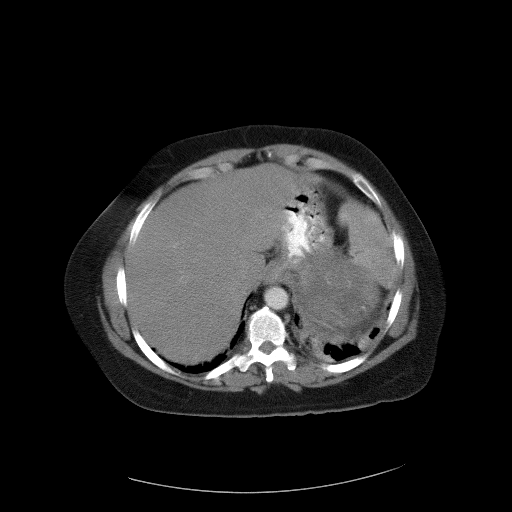
Contrast-enhanced abdominal CT, one axial slice; slice 84 of 90 in the series (ordered by position); reconstruction kernel FC01; 120 kVp; intravenous contrast given; soft-tissue window (W 400 / L 40 HU); 5 mm slice thickness; 512 × 512 image matrix. Female patient, age 55 years. From the clinical record (not read from this slice): diagnosis: adrenocortical carcinoma; tumour side: left adrenal; tumour size at pathology: 22 cm.
Structures marked on this image (semi-automatically segmented with operator editing):
- mass: bounding box <294,262,377,326> (left, top, right, bottom; pixels)